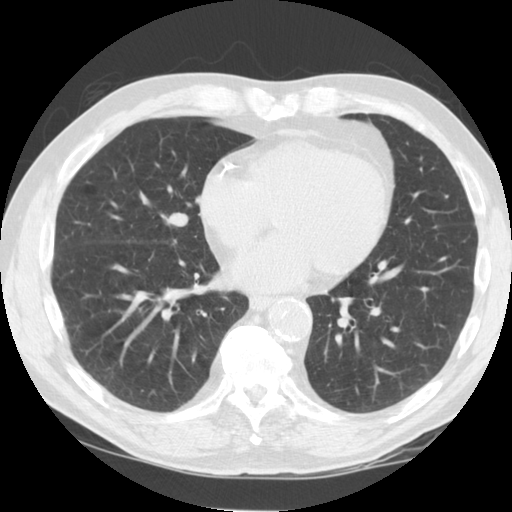
Axial slice from a low-dose chest CT screening exam; third screening round (two years after baseline); lung window (W 1500 / L -600 HU); 2.5 mm slice thickness; standard (soft-tissue) reconstruction kernel (STANDARD); 120 kVp; 512 × 512 image matrix. Male, age 64 years at enrolment. Current smoker at enrolment.
Expert-annotated lung lesion, box from (x=136, y=199) to (x=198, y=253) px. The exam's reader record, not a measurement of the box and not confirmed to be the same lesion: non-calcified nodule or mass ≥4 mm, right middle lobe, 21 × 14 mm, smooth margins, soft tissue attenuation, pre-existing on the prior screen: yes; interval growth: yes. Official screen result: positive, other. Lung cancer was diagnosed 74 days after this screen: non-small cell carcinoma, right middle lobe, poorly differentiated (G3), stage IIIA (AJCC 6th edition), 20 mm at pathology.